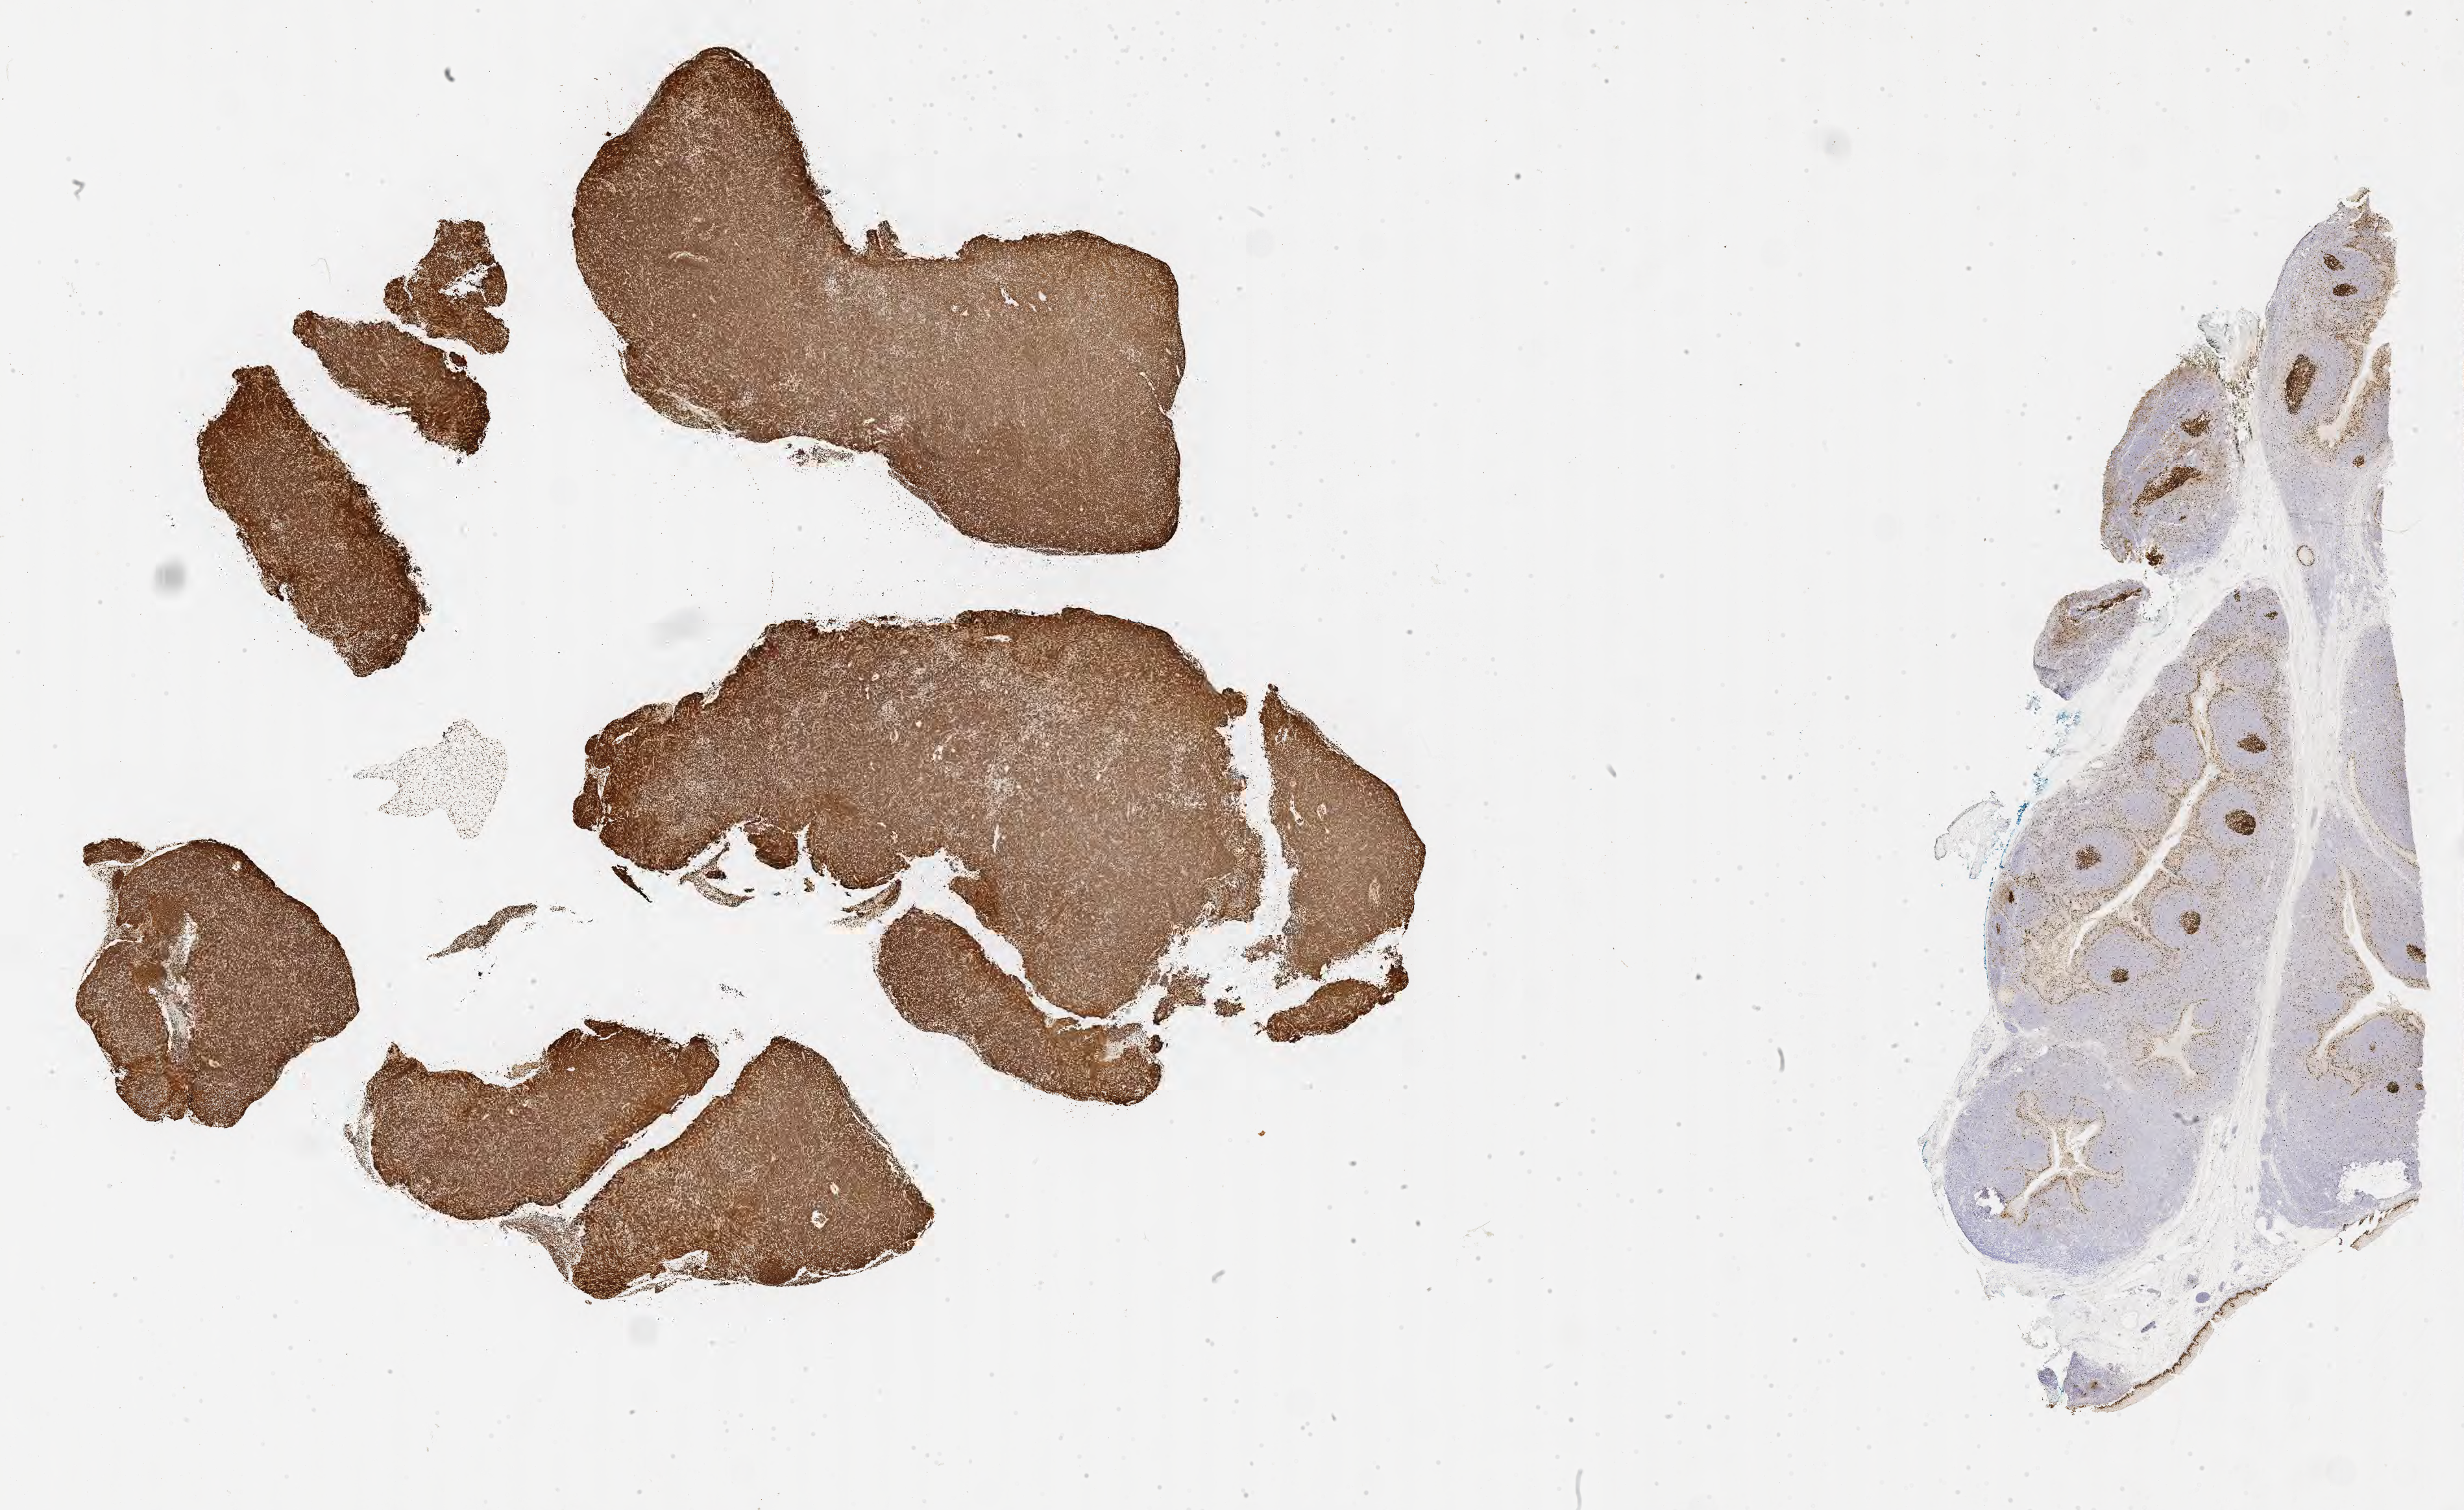
Immunohistochemistry (IHC) whole-slide image stained for Ki-67 — shown as a low-resolution overview of the whole scanned area (about 30.7 x 18.8 mm), specimen: tumor tissue, anatomic site: soft tissue. Female, age 9 years at initial diagnosis.
Histologic diagnosis: Burkitt lymphoma, NOS.